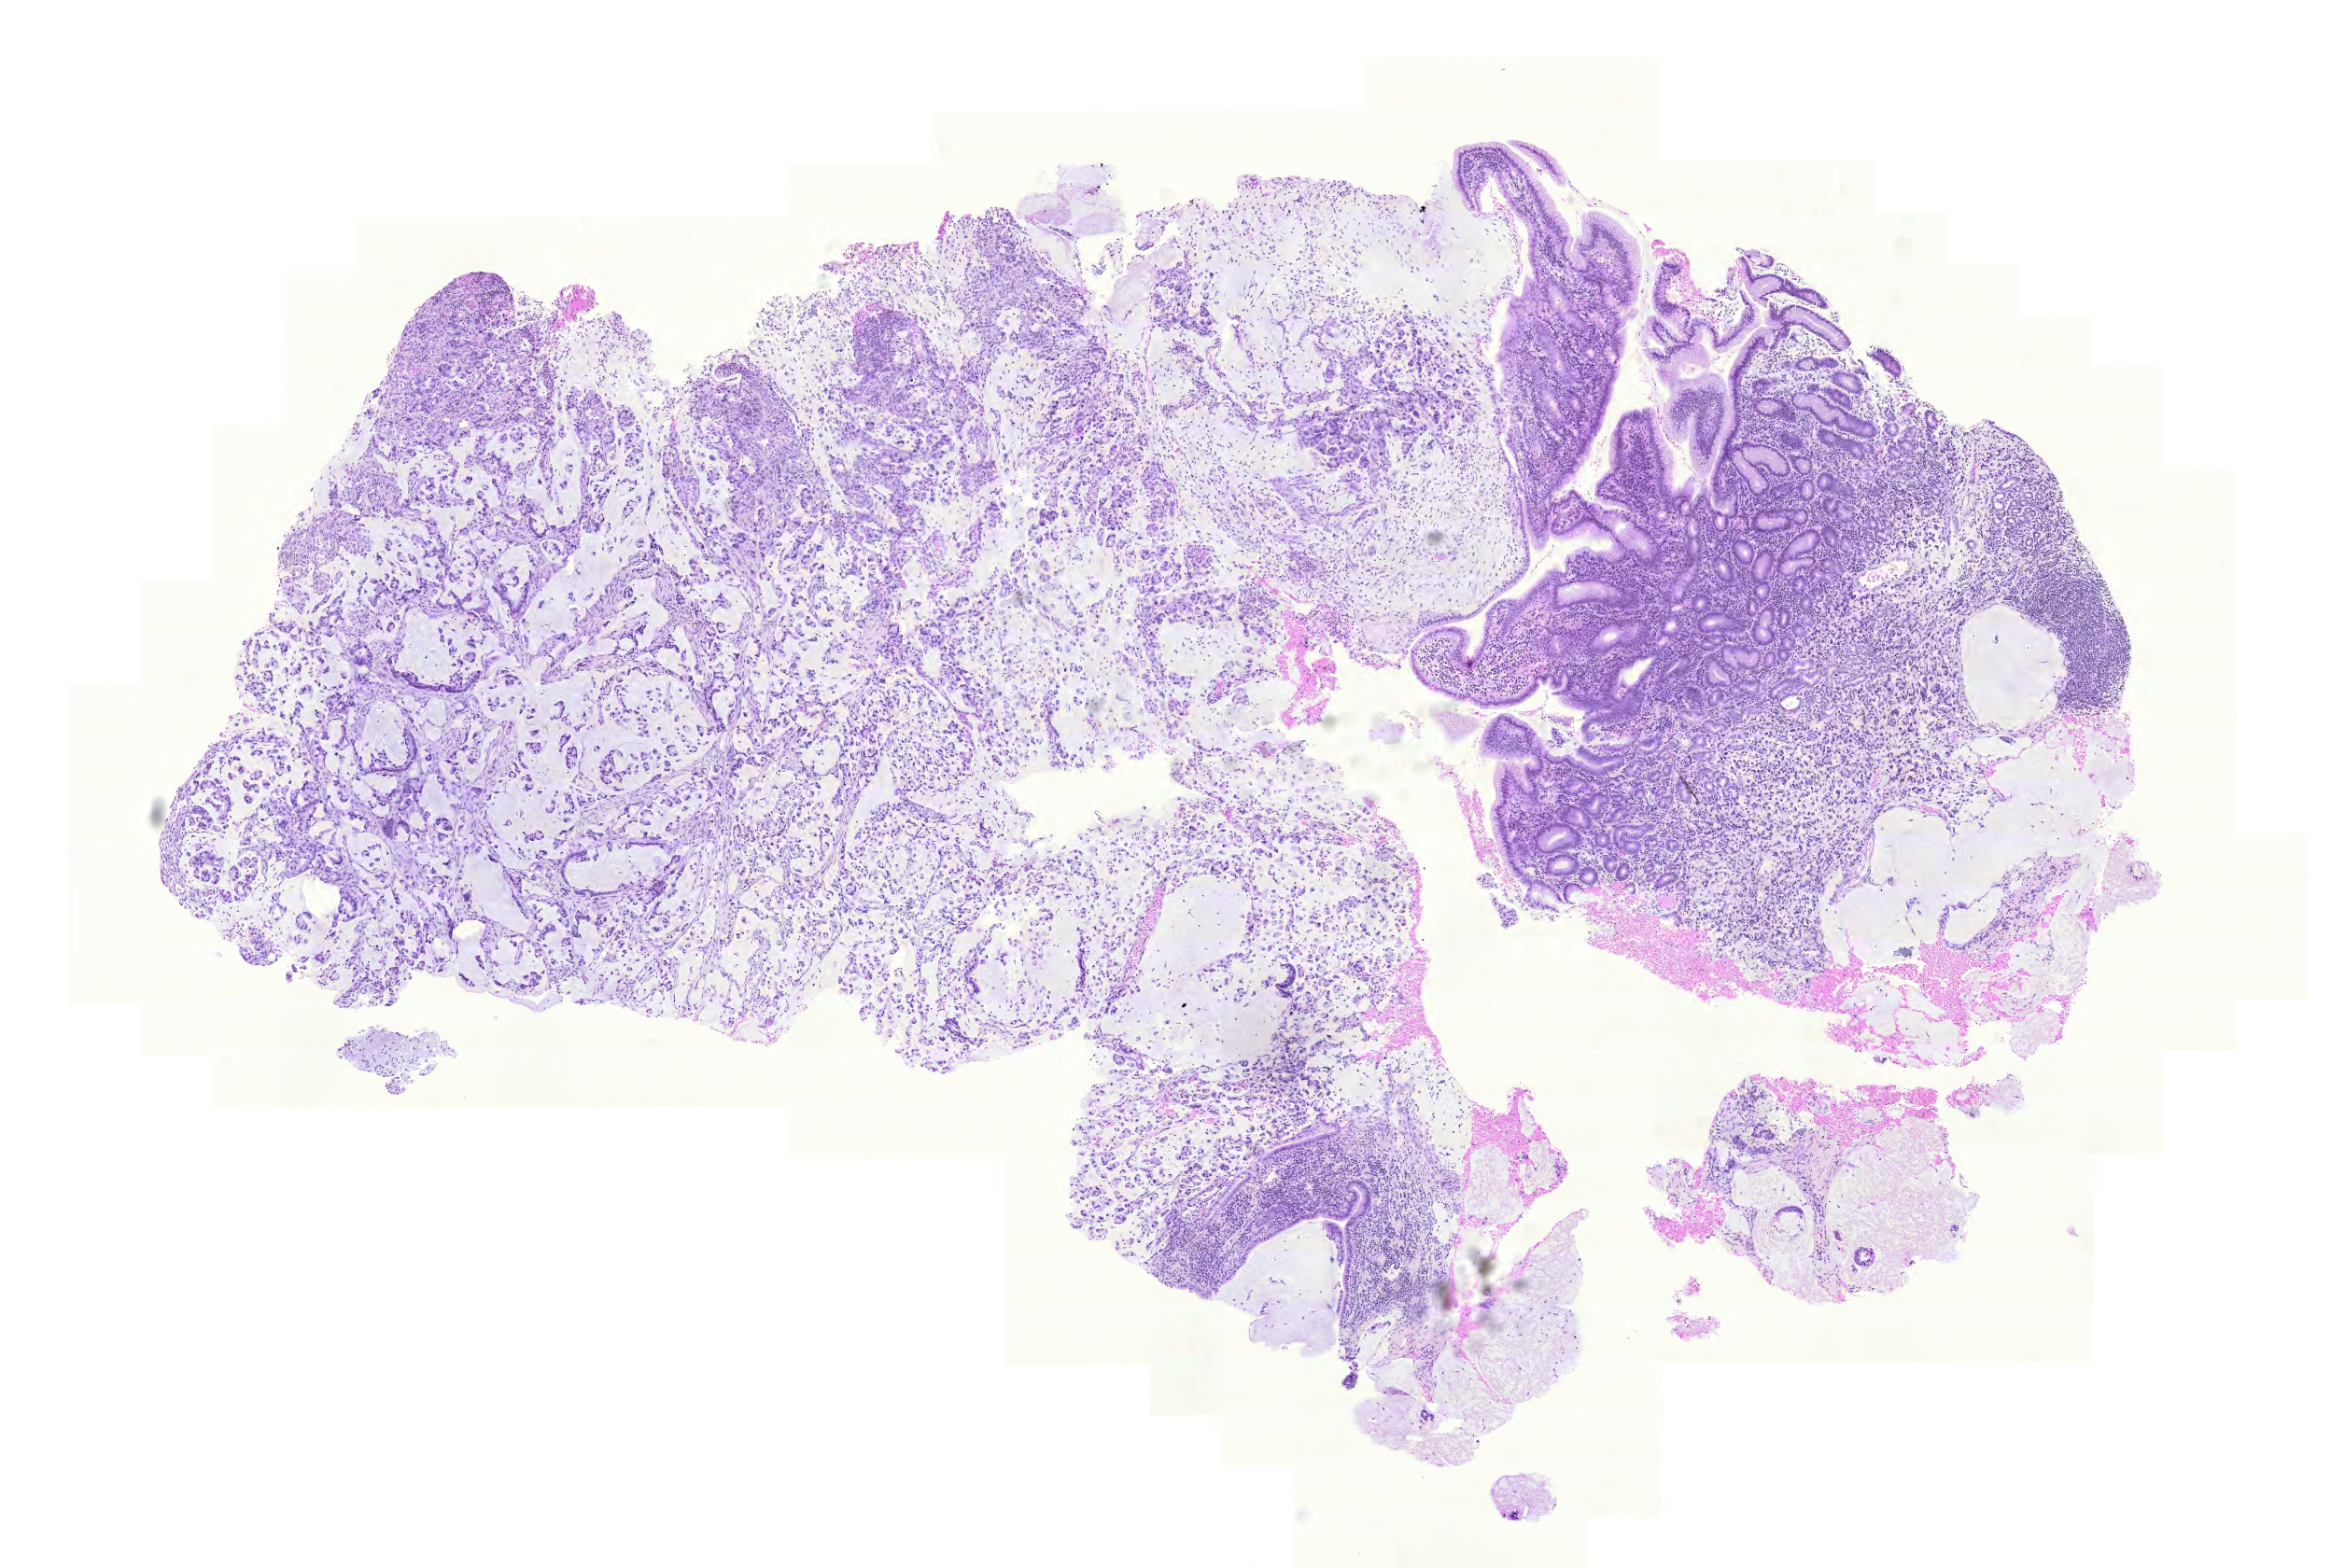
Whole-slide histology image, H&E, a low-resolution overview of the entire scanned area, about 9.3 x 6.2 mm (acquisition: 20x scan), formalin-fixed paraffin-embedded (FFPE) diagnostic section, sample: primary tumour, stomach. Male, age 72 years at initial diagnosis. Histologic grade: G3 (poorly differentiated).
- pathologic diagnosis: Mucinous adenocarcinoma
- AJCC pathologic stage: II (6th edition)